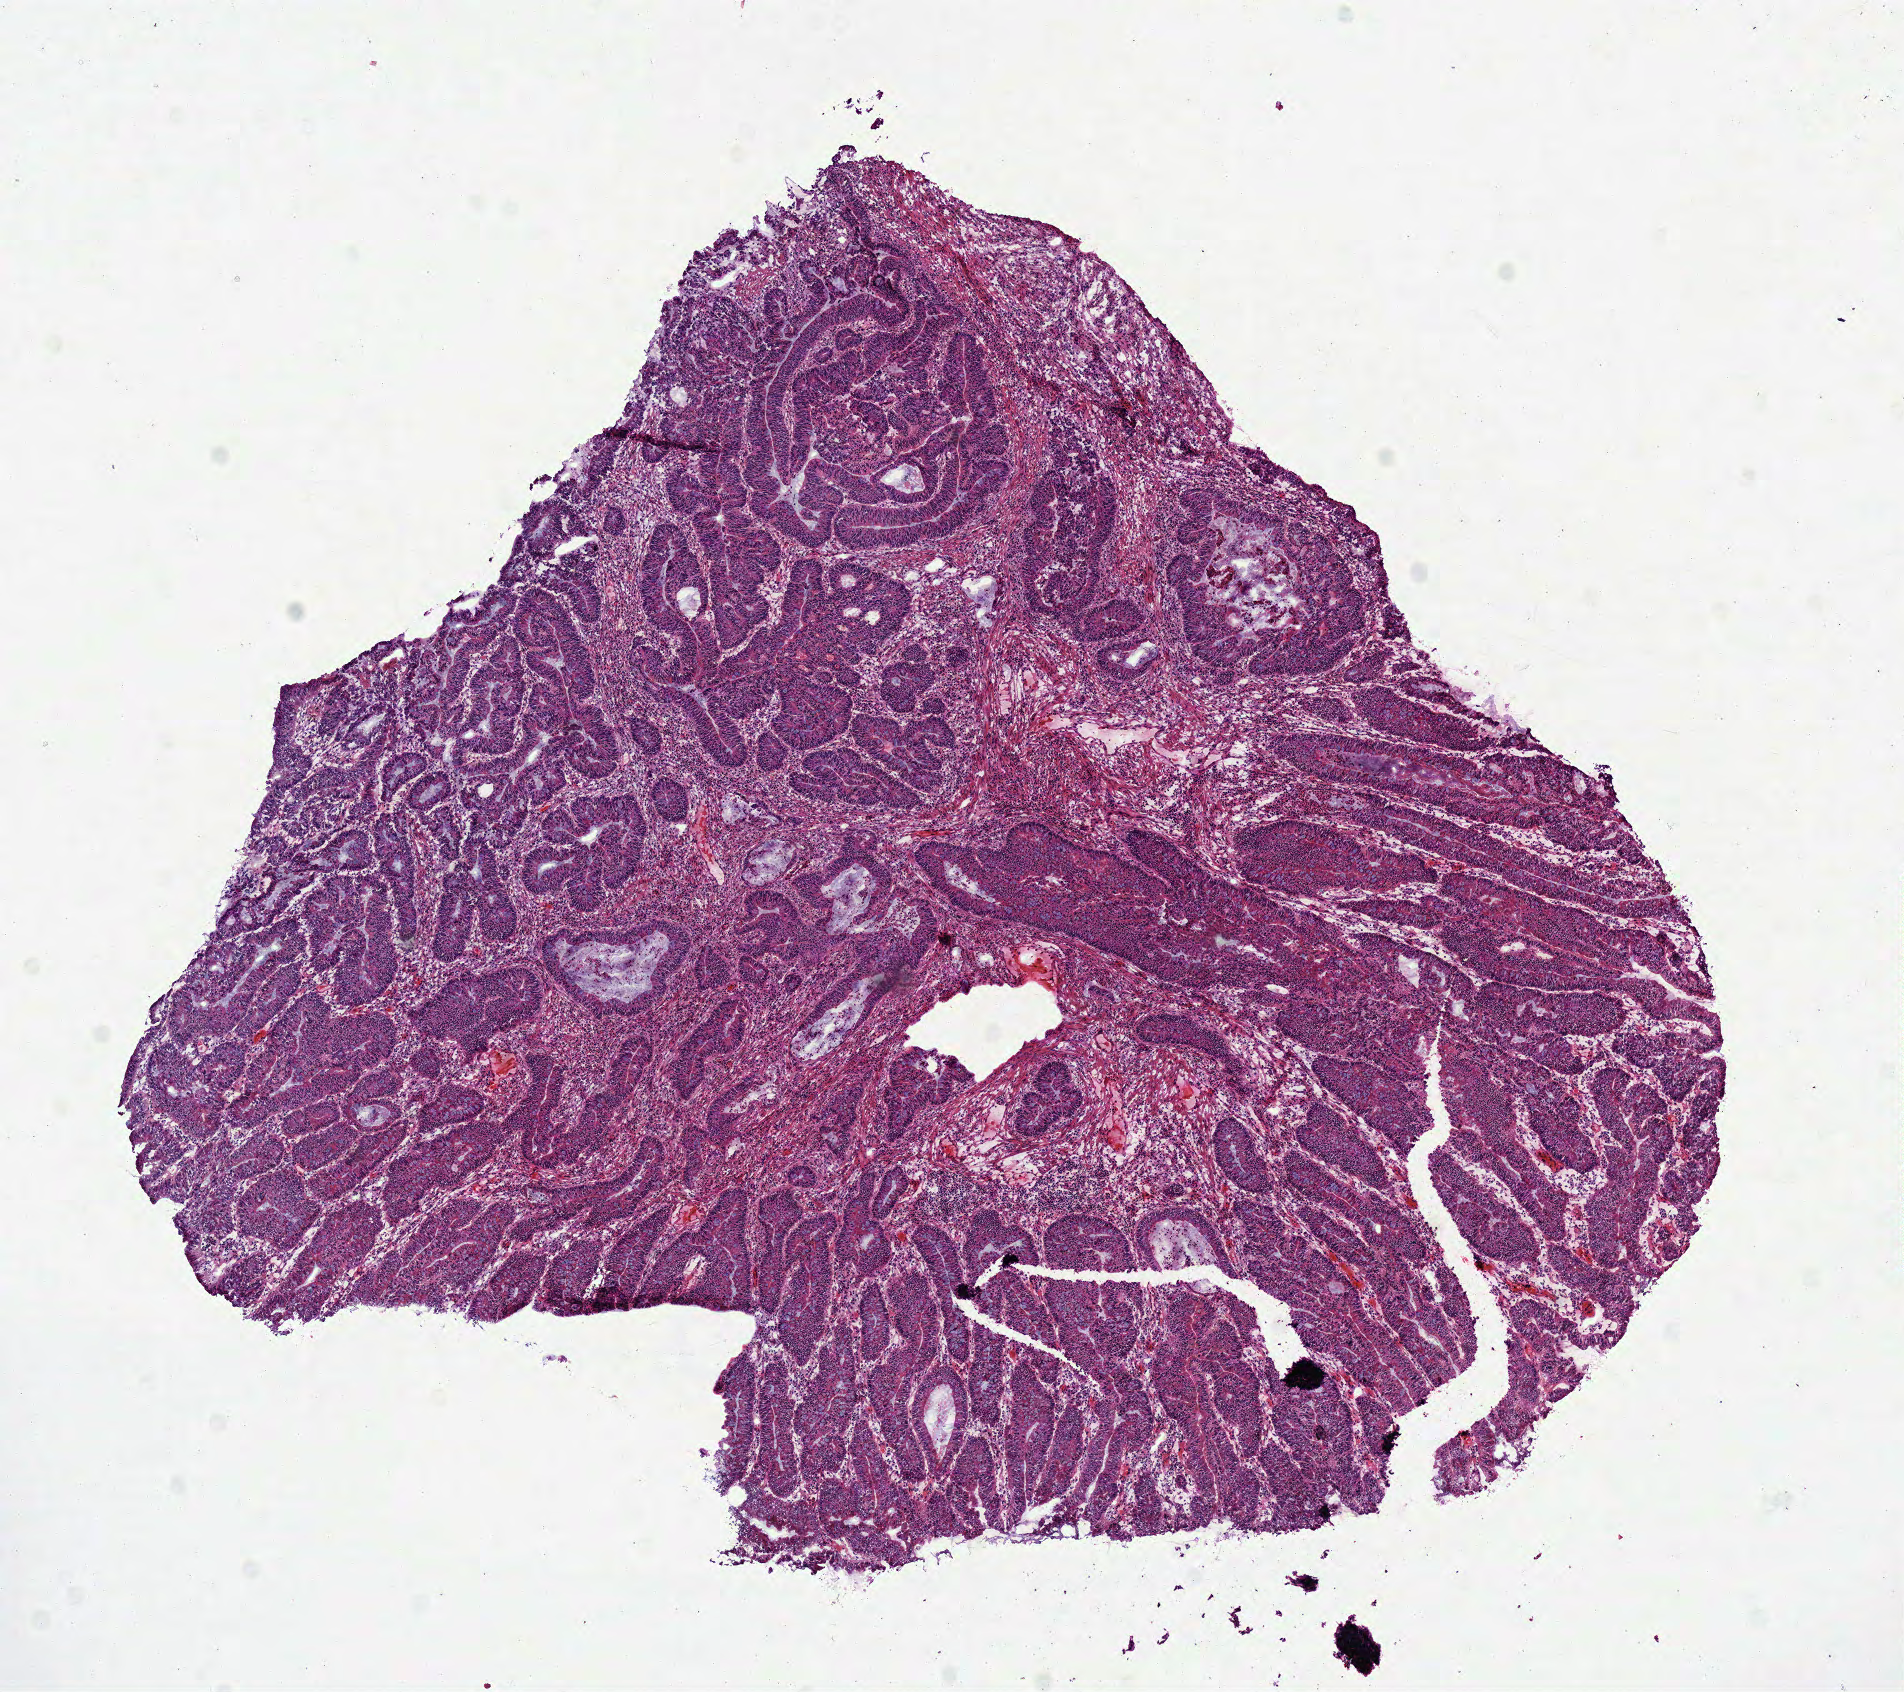
Digitized H&E-stained tissue section (whole slide) — low-resolution overview of the scanned area, about 7.5 x 6.7 mm, frozen section, sample: primary tumour, colon. Patient: female, age at initial diagnosis 46 years. Pathologist review of this section (percent, as recorded): tumour cells 80%, tumour nuclei 80%.
Pathologic diagnosis: Adenocarcinoma, NOS (sigmoid colon).